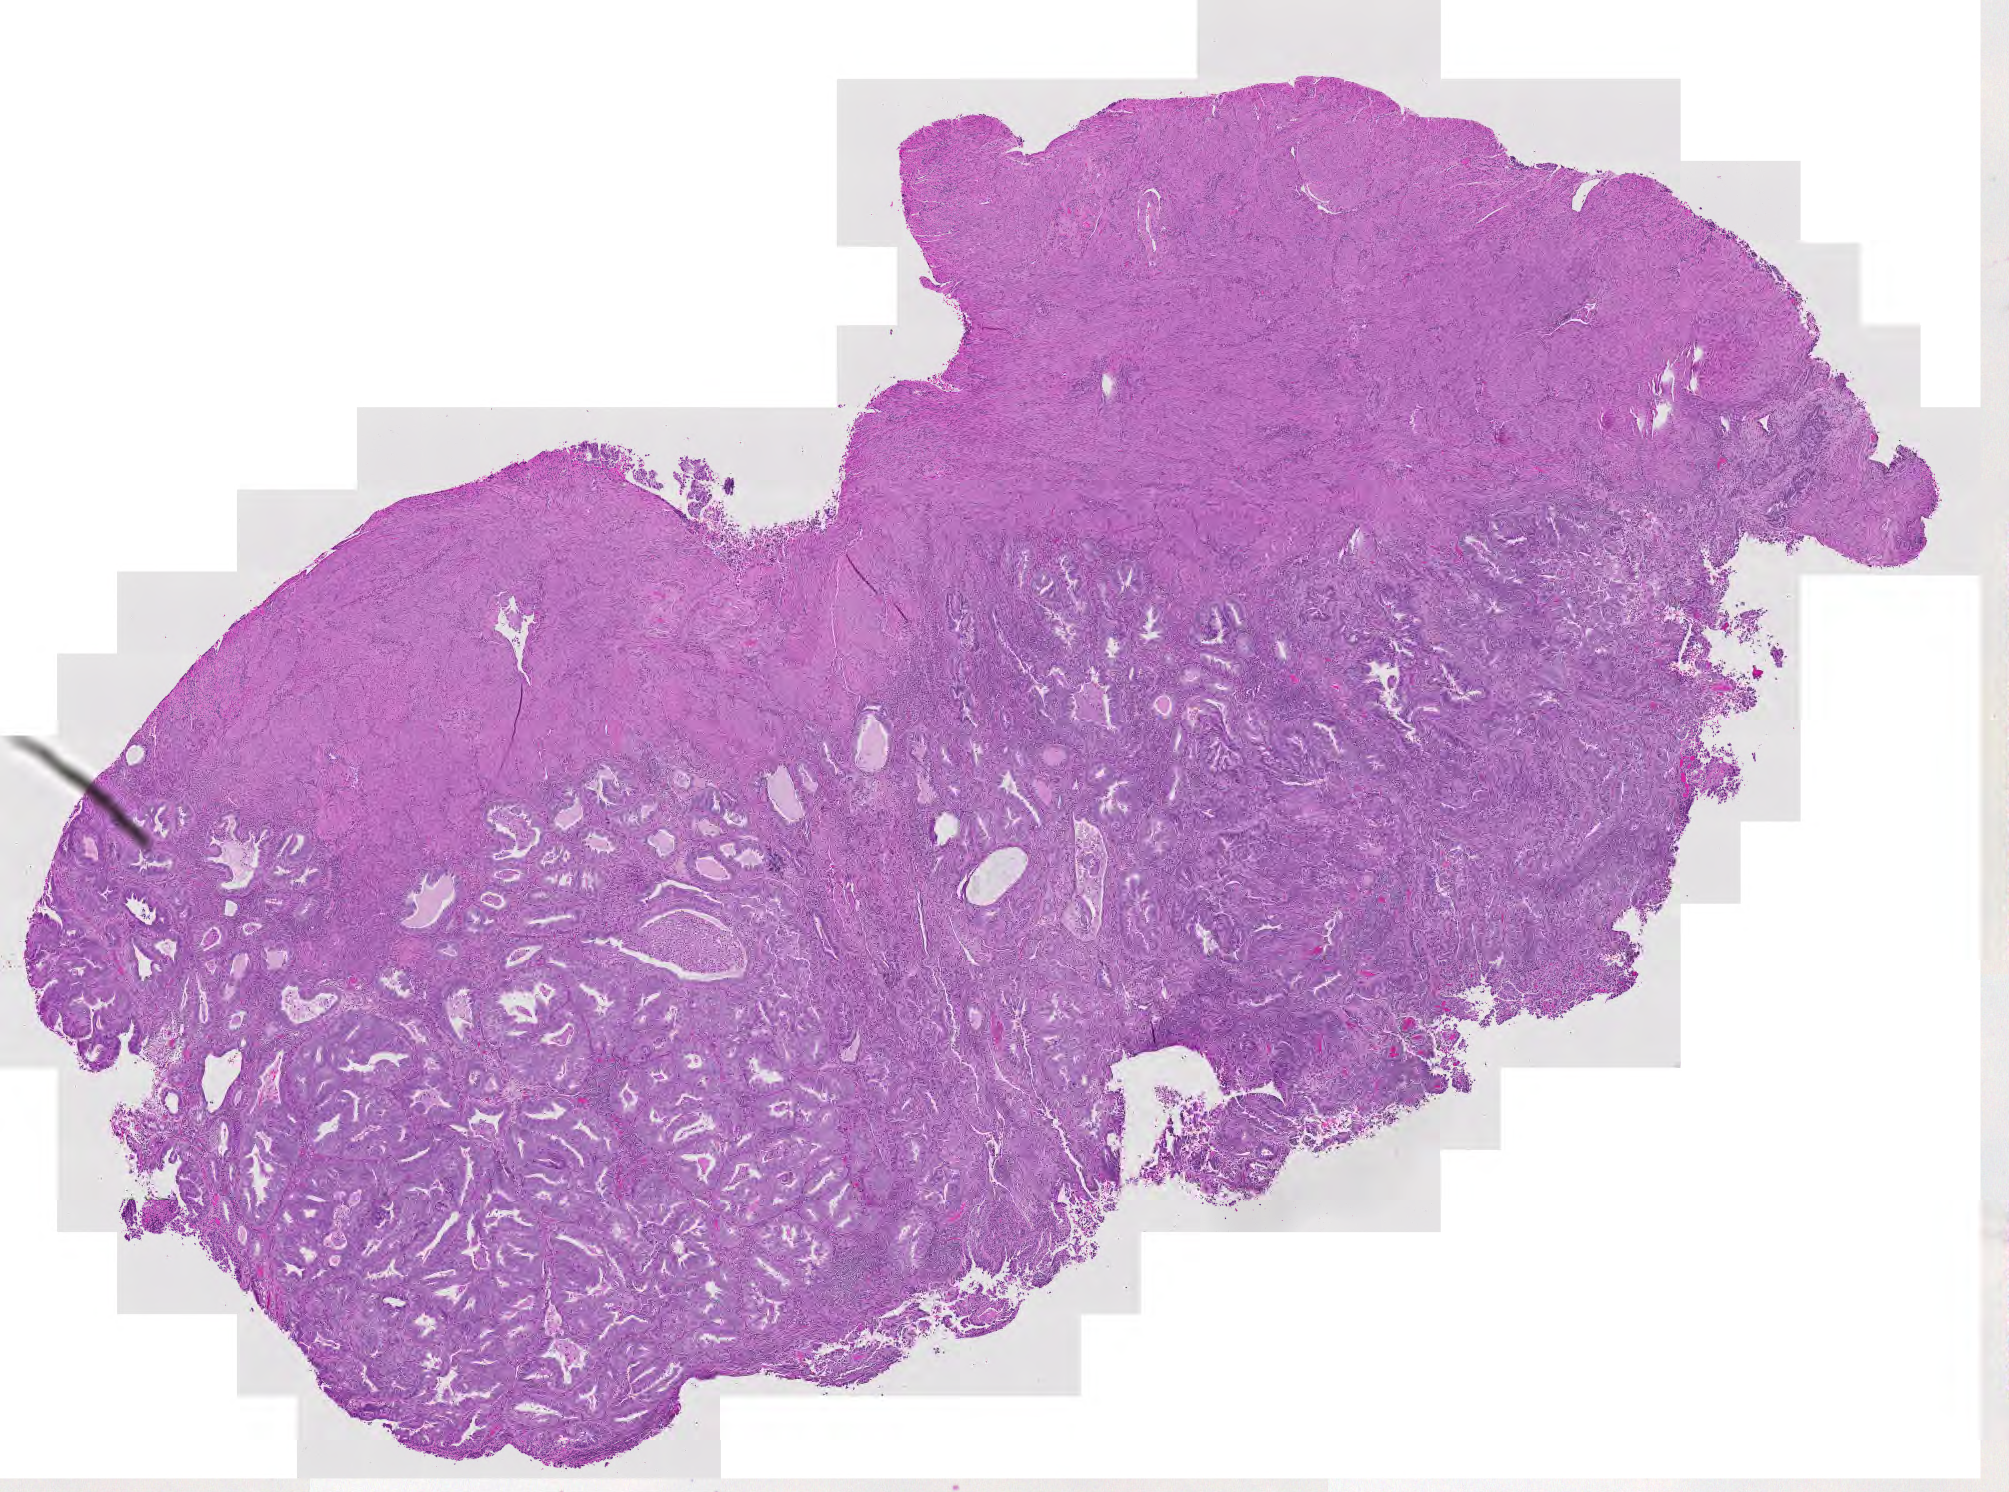
H&E-stained whole-slide image — a low-resolution overview of the entire scanned area, about 10.4 x 7.7 mm (from a 20x scan), tumour tissue sample, uterus. Patient: female, age 54 years. Histologic grade: G2 (moderately differentiated).
* histologic diagnosis: Endometrioid adenocarcinoma, NOS
* AJCC pathologic stage: I